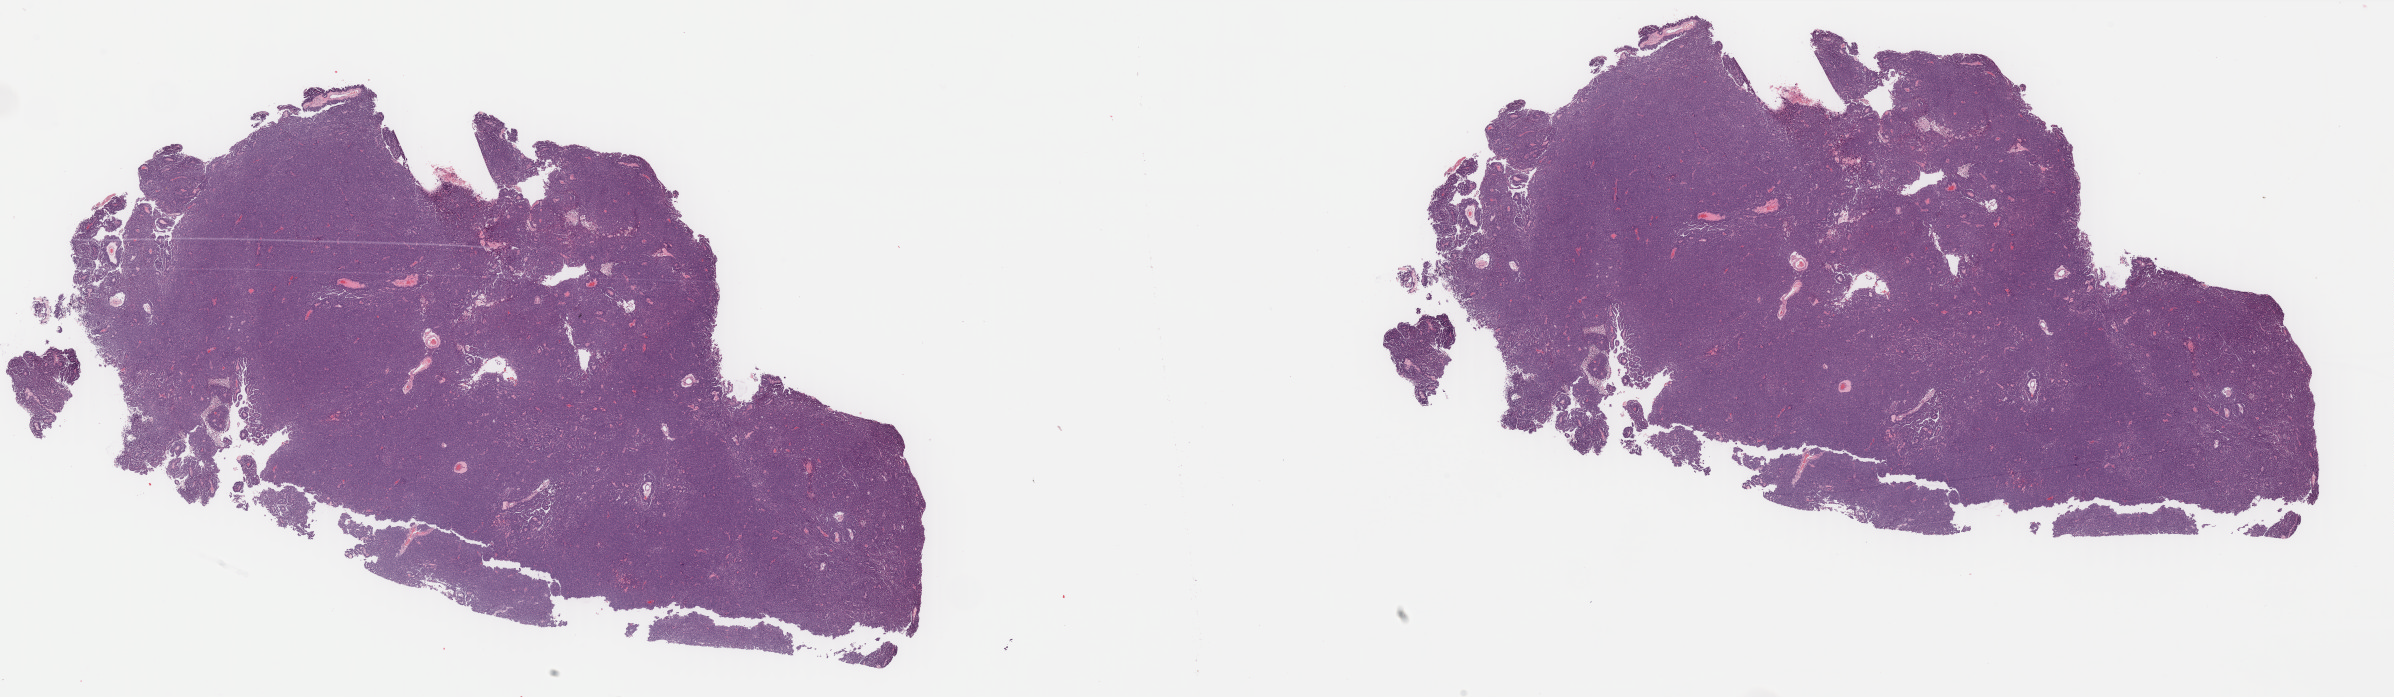
Digitized Hematoxylin and eosin (H&E) stained tissue section (whole slide), shown as a low-resolution overview of the whole scanned area (about 37.9 x 11.0 mm), FFPE section, sample: primary tumour, ovary. Female patient; age at initial diagnosis 78 years. Histologic grade: G3 (poorly differentiated).
FIGO stage: IIA. Pathologic diagnosis: Serous cystadenocarcinoma, NOS.